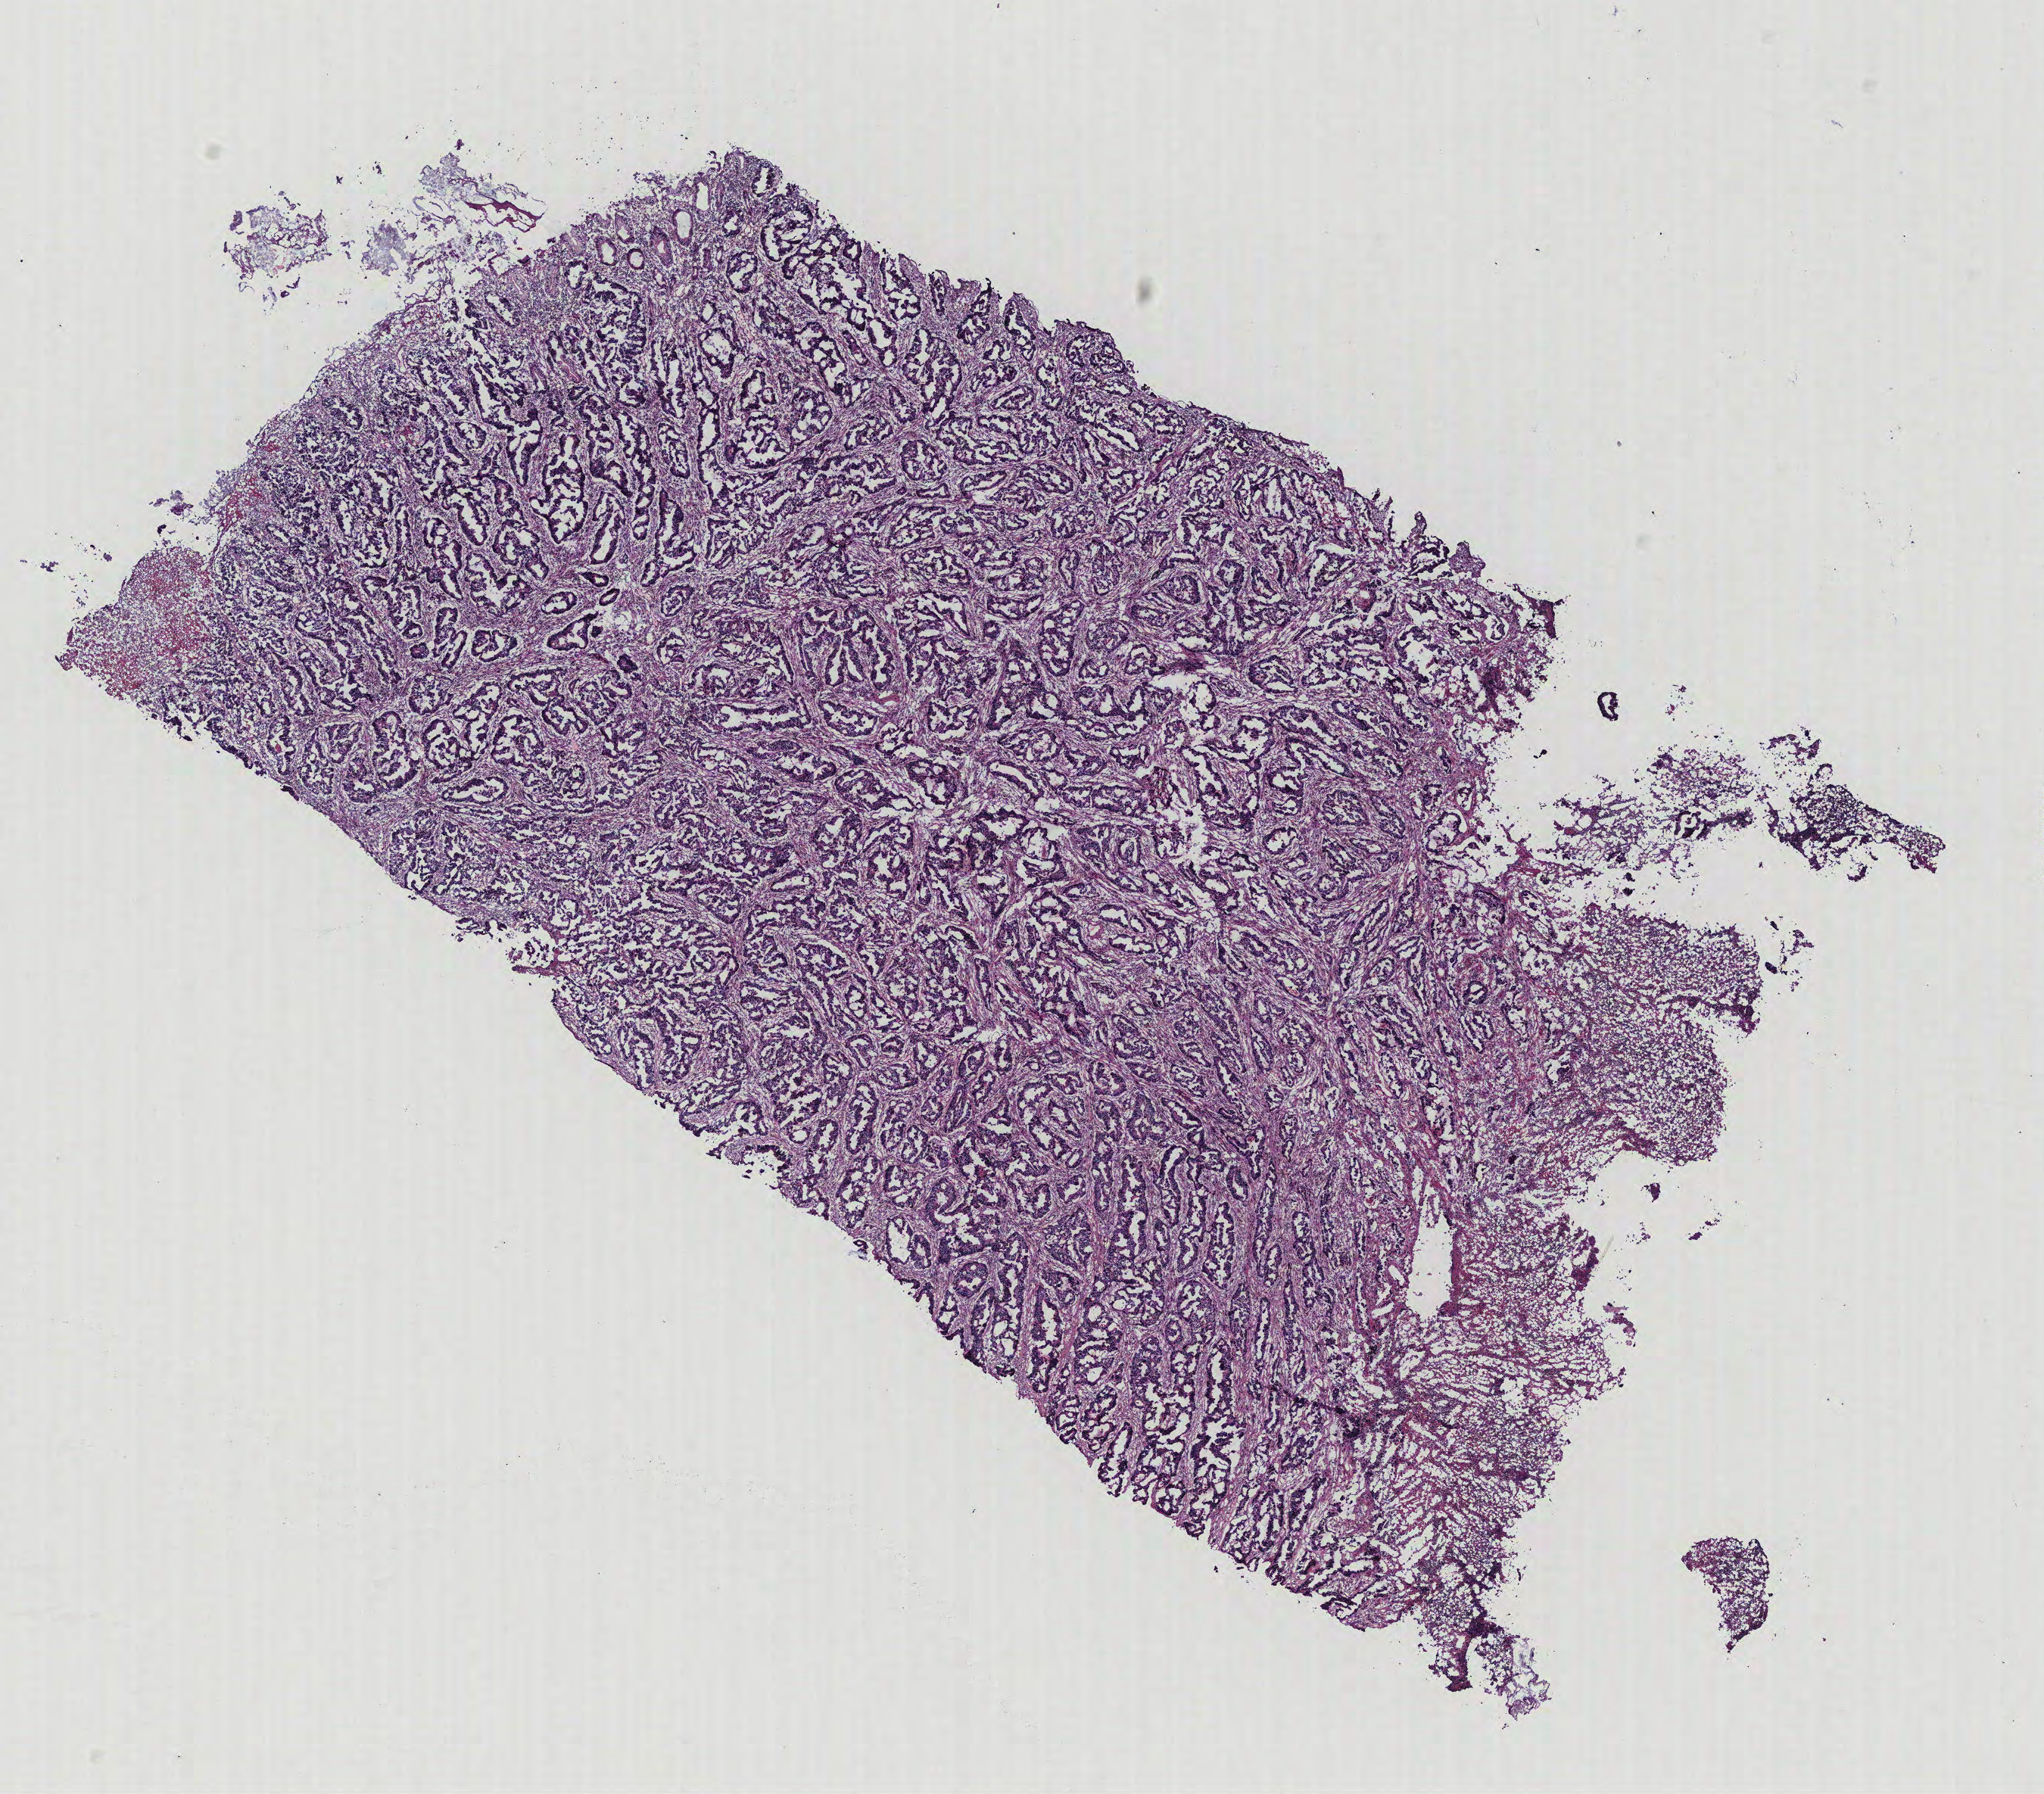
H&E-stained whole-slide image, shown as a low-resolution overview of the whole scanned area (about 10.8 x 9.5 mm, from a 40x scan). Colon, normal (non-tumour) tissue. 76-year-old male patient.
This section: normal (non-tumour) tissue from the same patient. Patient diagnosis: Adenocarcinoma, NOS.